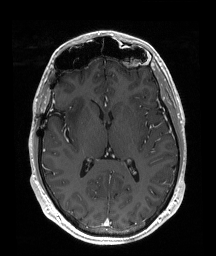
Brain MRI from a brain-tumour surgery series, one axial slice; position 101 of 192 along the scan axis; T1-weighted post-contrast; 216 × 256 image matrix, field of view 219 × 260 mm. From the clinical record (not read from this slice): histopathology: Astrocytoma; WHO grade: 2; IDH mutation: yes; tumour location: Right Insular.
Annotated regions visible in this slice (expert manual segmentation):
- tumour: box from (x=66, y=97) to (x=86, y=127) px